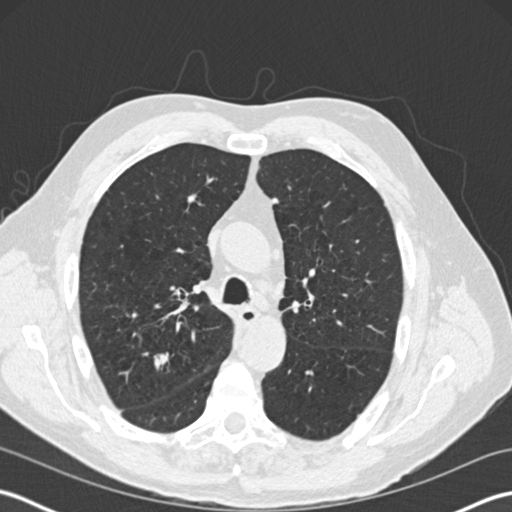
Chest CT (low-dose screening protocol), one axial image, third screening round (two years after baseline), lung window (W 1500 / L -600 HU), 512 × 512 image matrix. Male, age 65 years at enrolment. Former smoker at enrolment.
- Expert-annotated lung lesion, bounding box <141,348,182,384> (left, top, right, bottom; pixels).
- The screening reader recorded 6 non-calcified nodules or masses ≥4 mm on this exam; which of them this box marks is not recorded.
- Participant outcome: lung cancer diagnosed 78 days after this screen — adenocarcinoma, NOS, right upper lobe, moderately differentiated (G2), stage IA (AJCC 6th edition), 16 mm at pathology.